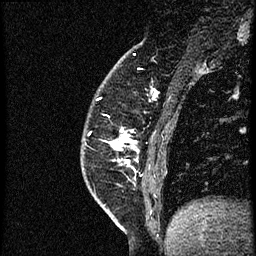
Breast MRI (dynamic contrast-enhanced), one sagittal slice; slice 17 of 56 in the series (ordered by position); dynamic contrast-enhanced study with each time point stored as its own series, time point 2 of 4 at this slice position (early post-contrast, ordered by acquisition time); 1.5 T; TE 4.2 ms, TR 18.9 ms; 256 × 256 image matrix, field of view 200 × 200 mm. Female patient. From the clinical record (not read from this slice): setting: breast cancer imaged before/during neoadjuvant chemotherapy; receptor status: HER2-positive.
Outlined on this slice (semi-automatically segmented with operator editing):
- analysis volume of interest (the breast-tissue region the enhancement analysis was run in; not a lesion): bounding box [x1, y1, x2, y2] px = [111, 87, 174, 189]
- tumour enhancement mask (voxels above the 100 % enhancement threshold inside the analysis volume of interest): [112, 130, 139, 162]